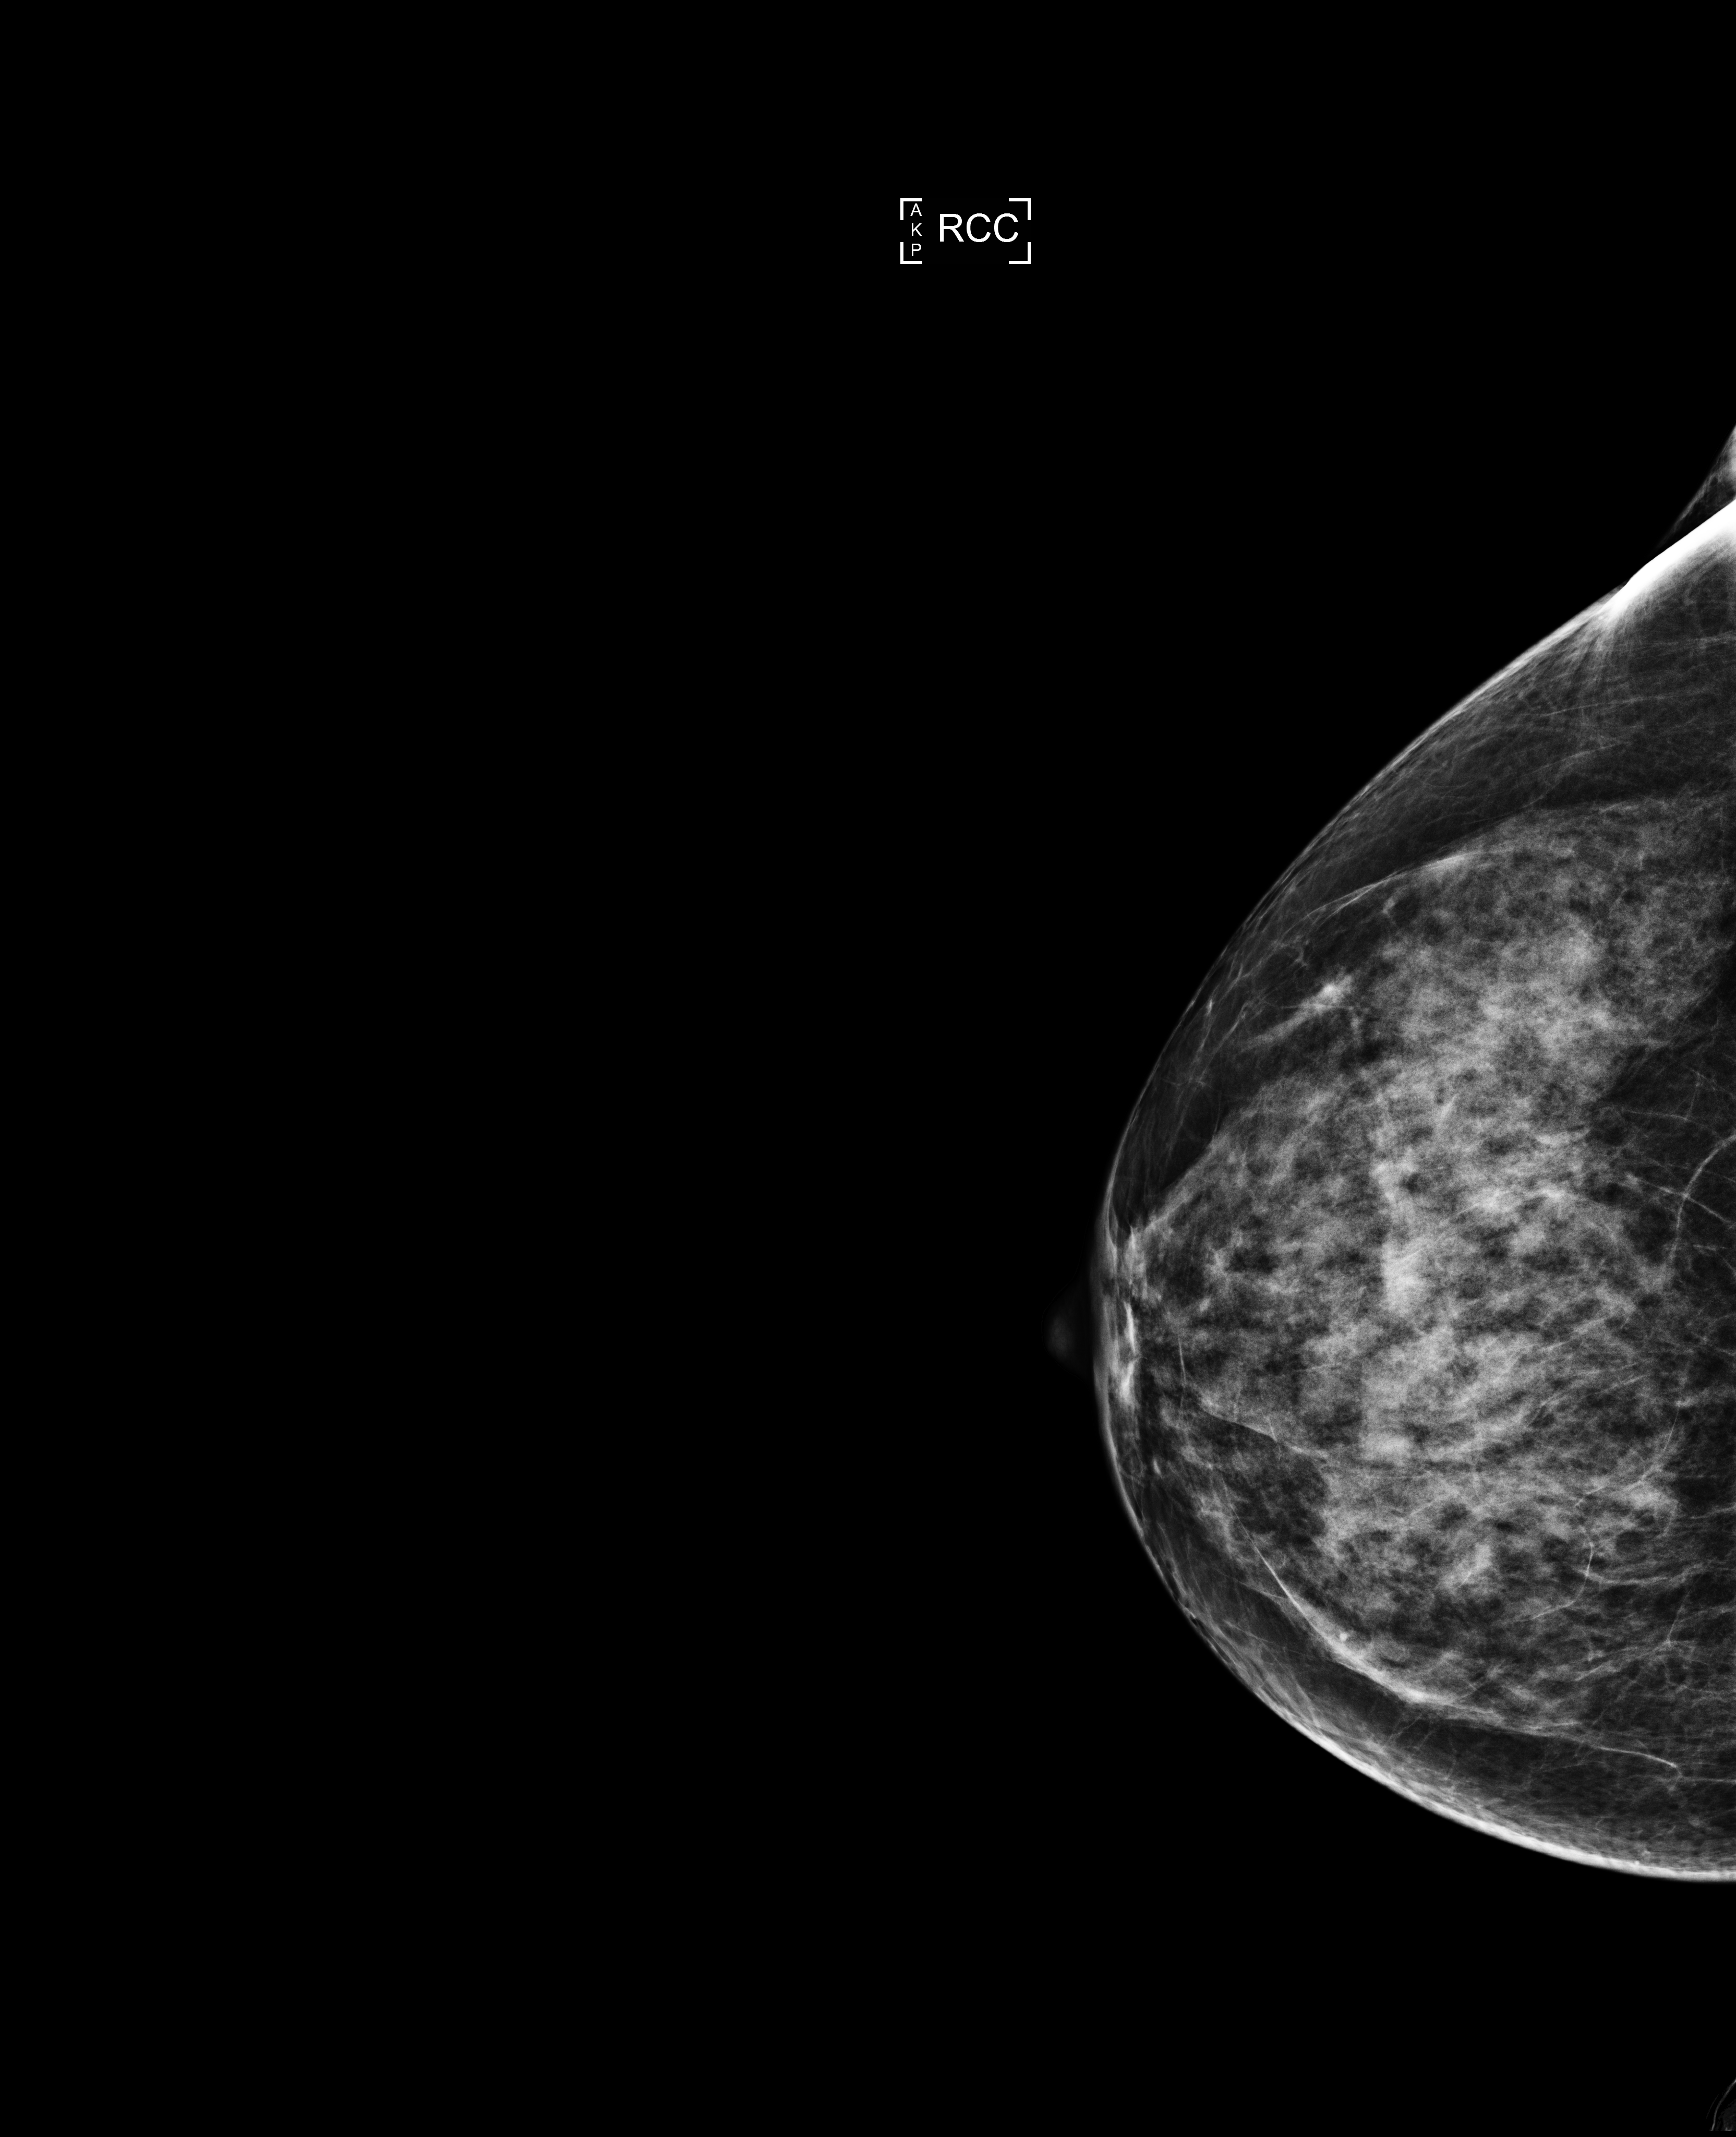
Screening examination; compressed breast thickness 54 mm; system: Selenia Dimensions. Female patient, age 52 years.
Image type: full-field digital mammogram. Breast: right. Projection: craniocaudal (CC) view.